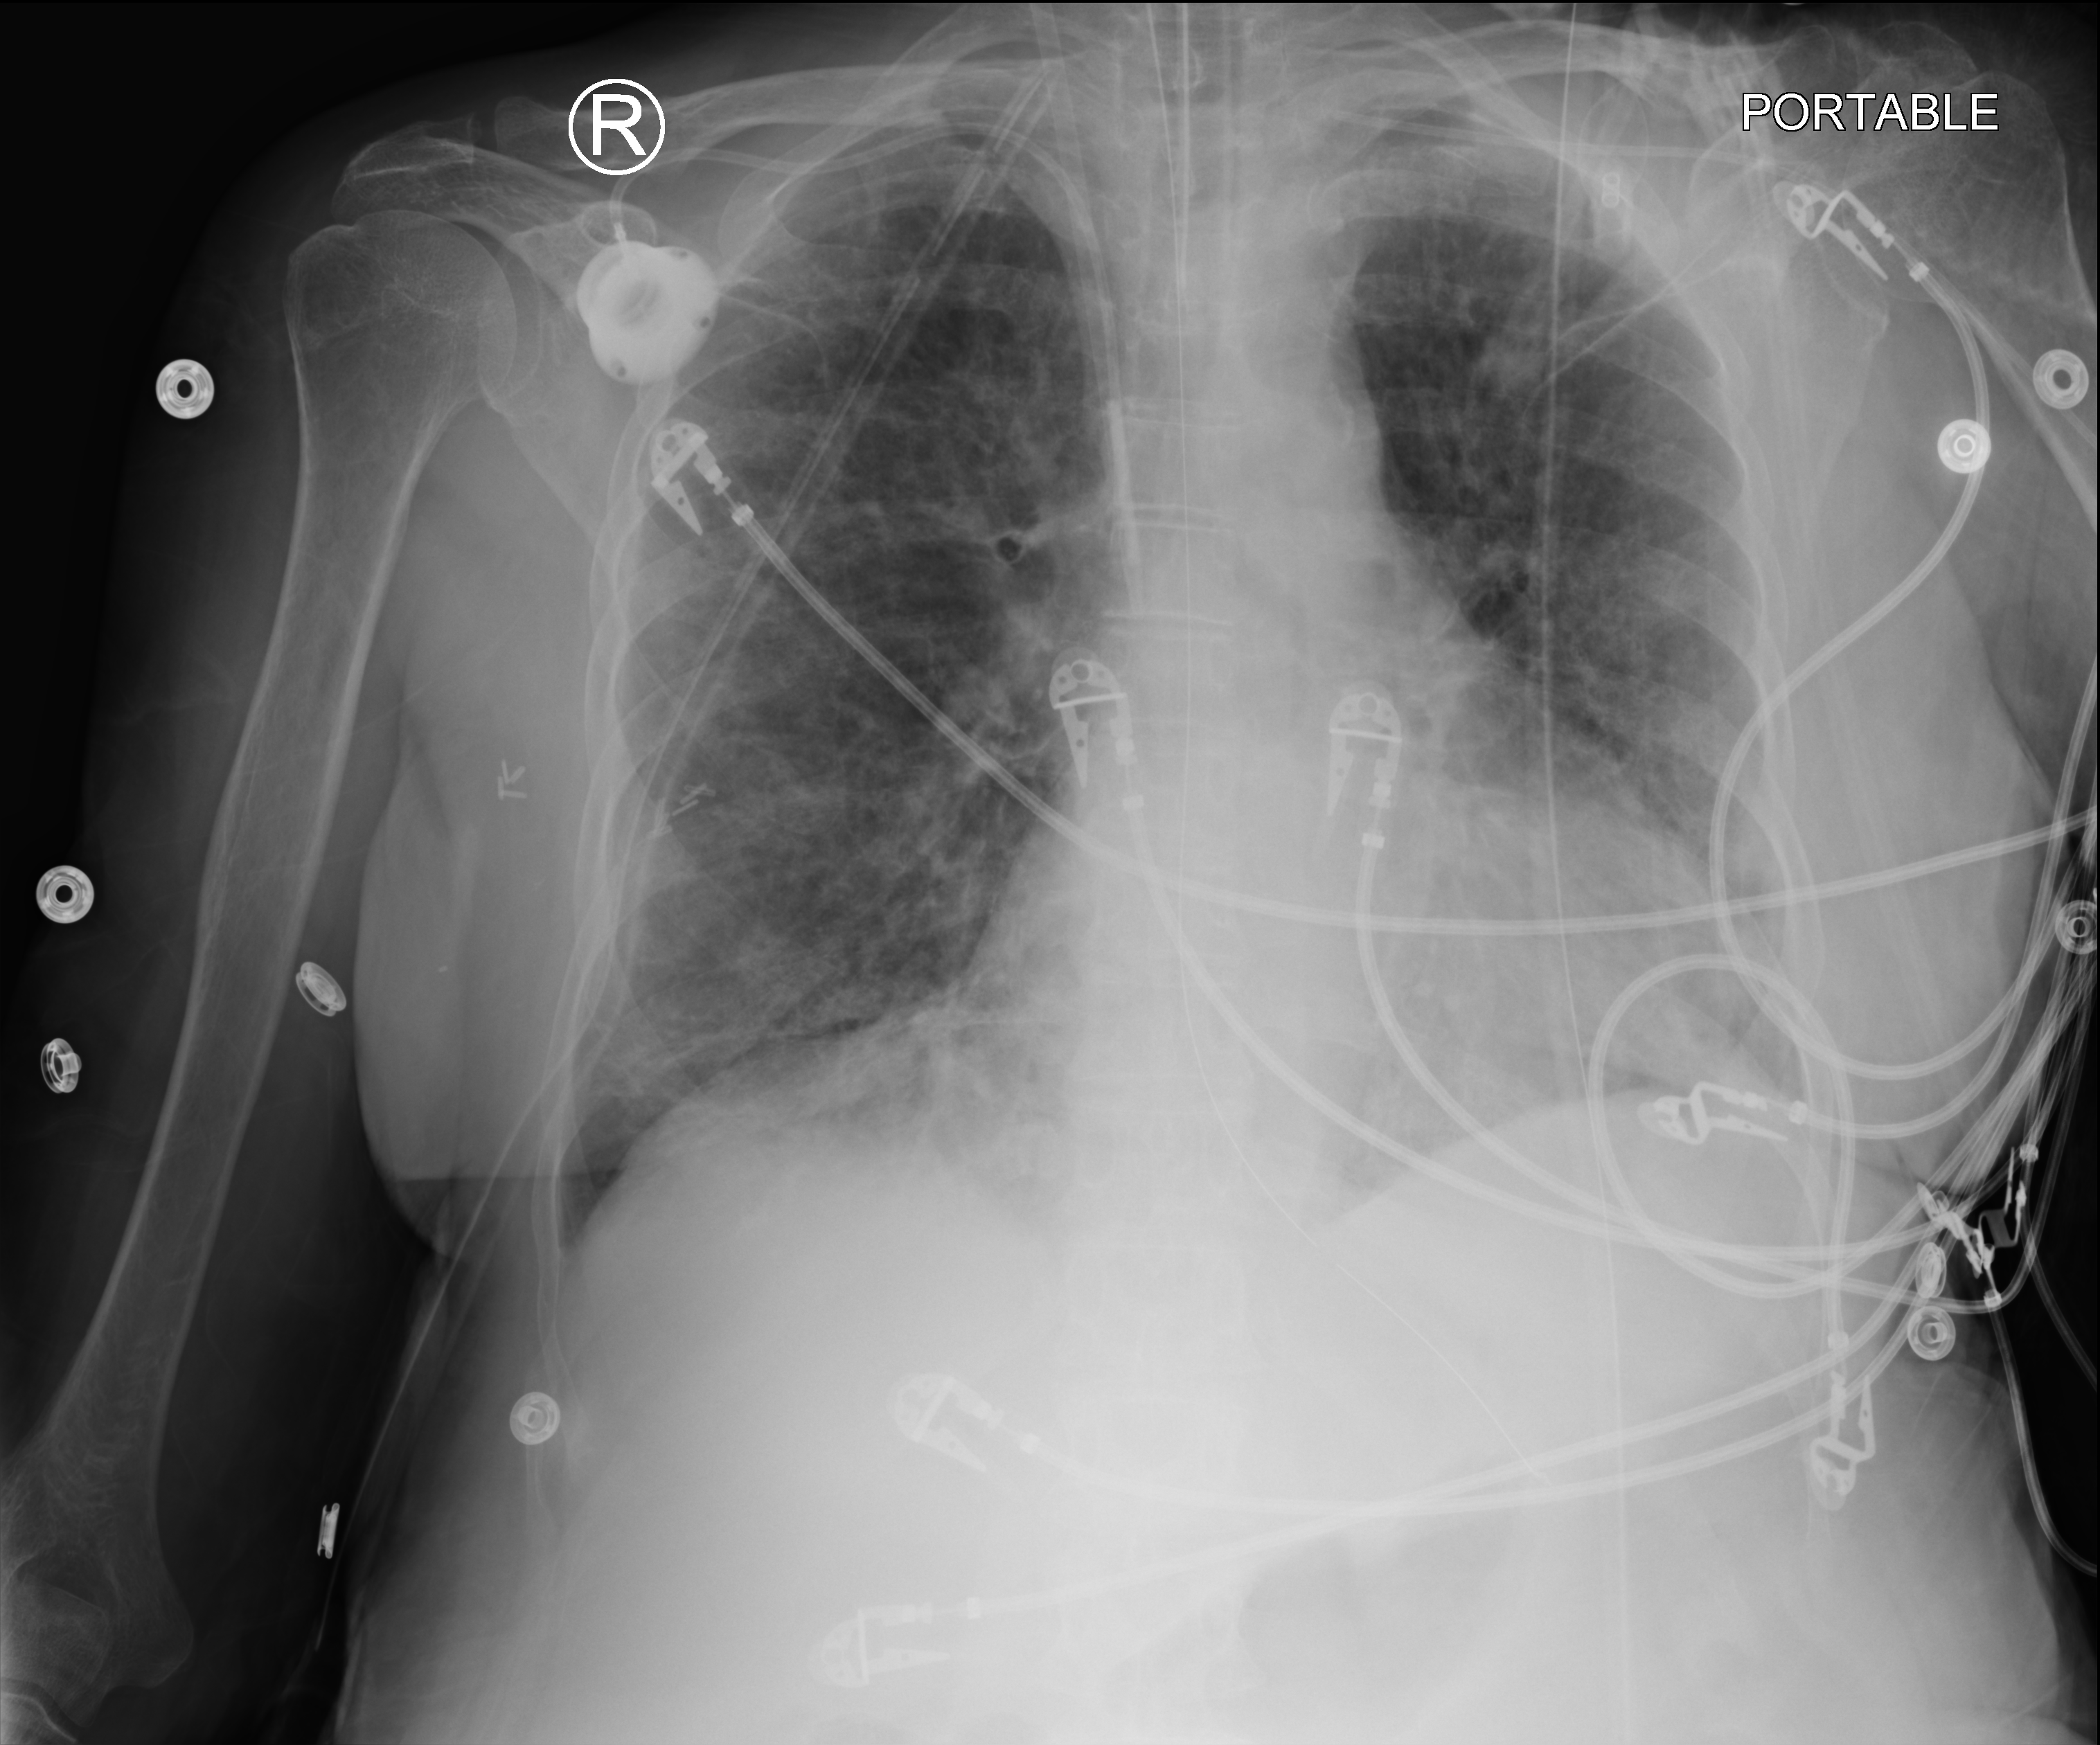
Chest X-ray (portable); anteroposterior (AP) projection. Female patient hospitalised with COVID-19, age 60–74 years.
Hospital-stay facts (about this admission, not read from this image; timing relative to this image not recorded): admitted to intensive care during this hospital stay: yes; mechanically ventilated during this hospital stay: yes.